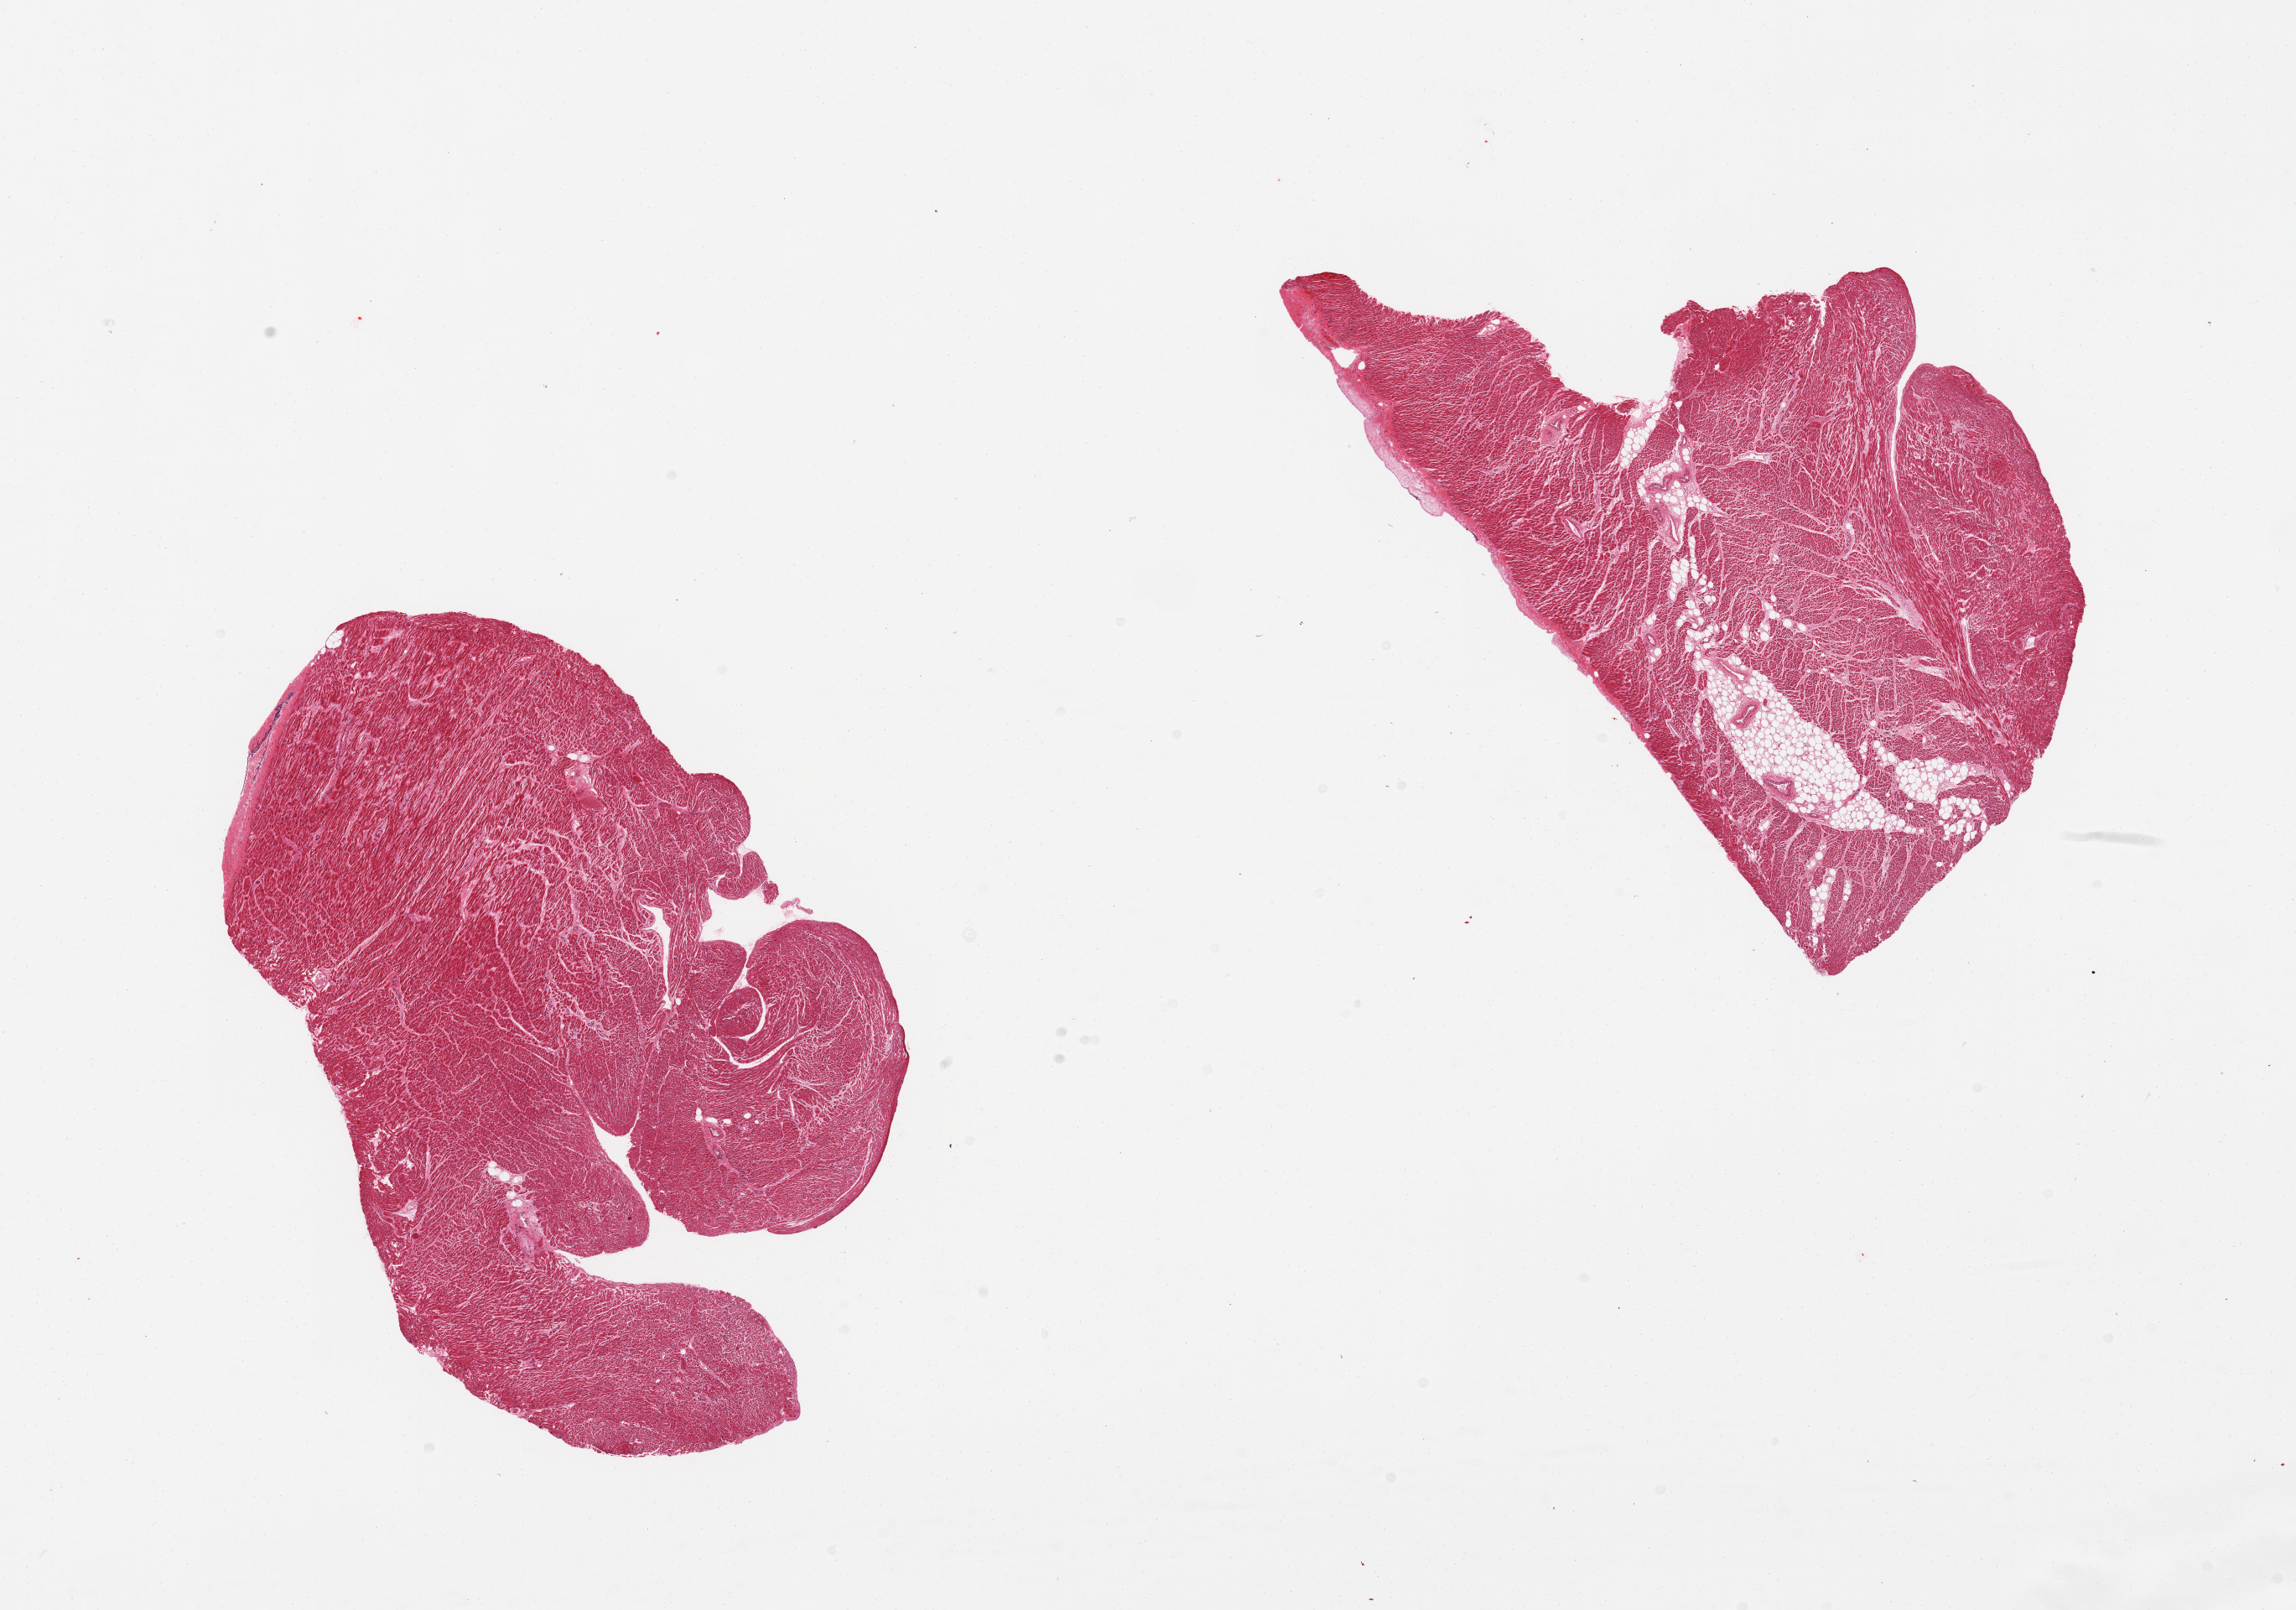
Digitized haematoxylin and eosin-stained section — a low-resolution overview of the entire scanned area, about 21.7 x 15.2 mm, PAXgene-fixed, paraffin-embedded tissue, target tissue: heart, tissue donor sample. Donor sex: male.
• reviewer comment on this tissue sample: 2 pieces, patchy interstitial fibrosis, moderate